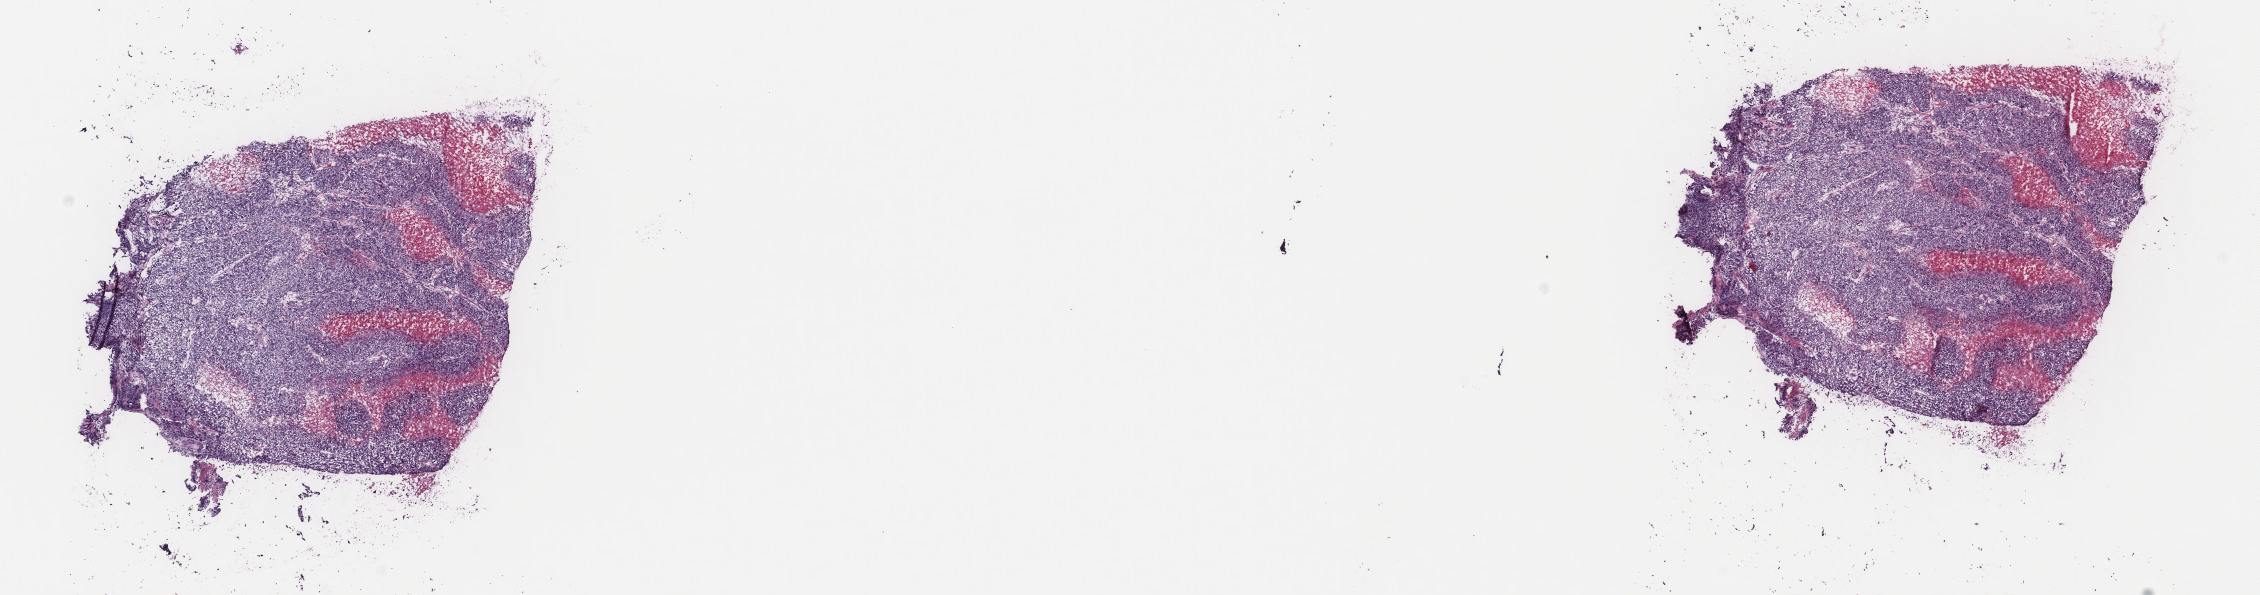
Whole-slide histology image, H&E-stained — a low-resolution overview of the entire scanned area, about 17.9 x 4.7 mm (slide scanned at 40x). Frozen section from the top of the tissue portion. Uterus, primary tumour sample. Patient: female, age at initial diagnosis 69 years. Histologic grade: G3 (poorly differentiated). Slide review estimates, as recorded: tumour cells 75%, tumour nuclei 95%, normal cells 0%, stromal cells 5%, necrosis 20%. Infiltration values recorded for this section: lymphocyte infiltration 5%, monocyte infiltration 3%, neutrophil infiltration 8%.
Diagnosis: Endometrioid adenocarcinoma, NOS (endometrium). FIGO stage: IB.